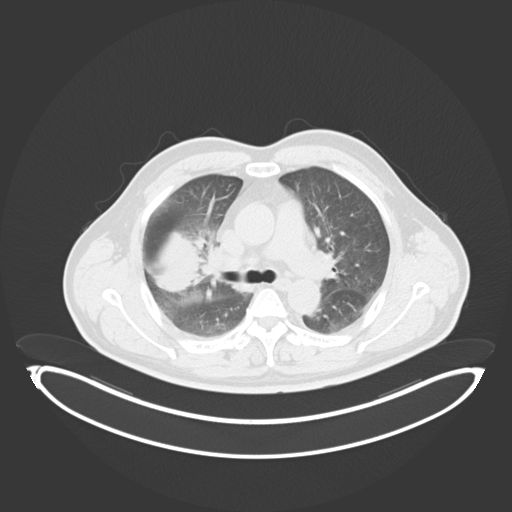
Chest CT, one axial slice; slice 216 of 284 in the series (ordered by position); reconstruction kernel B30f; lung window (W 1500 / L -600 HU); 3 mm slice thickness; 512 × 512 image matrix, field of view 500 × 500 mm. Male patient, age 55 years. From the clinical record (not read from this slice): clinical TNM (as recorded): T3 N2 M1.
Outlined on this slice (bounding box drawn by a radiologist):
- lung tumour (recorded histology: adenocarcinoma): bounding box [x1, y1, x2, y2] px = [142, 223, 204, 294]